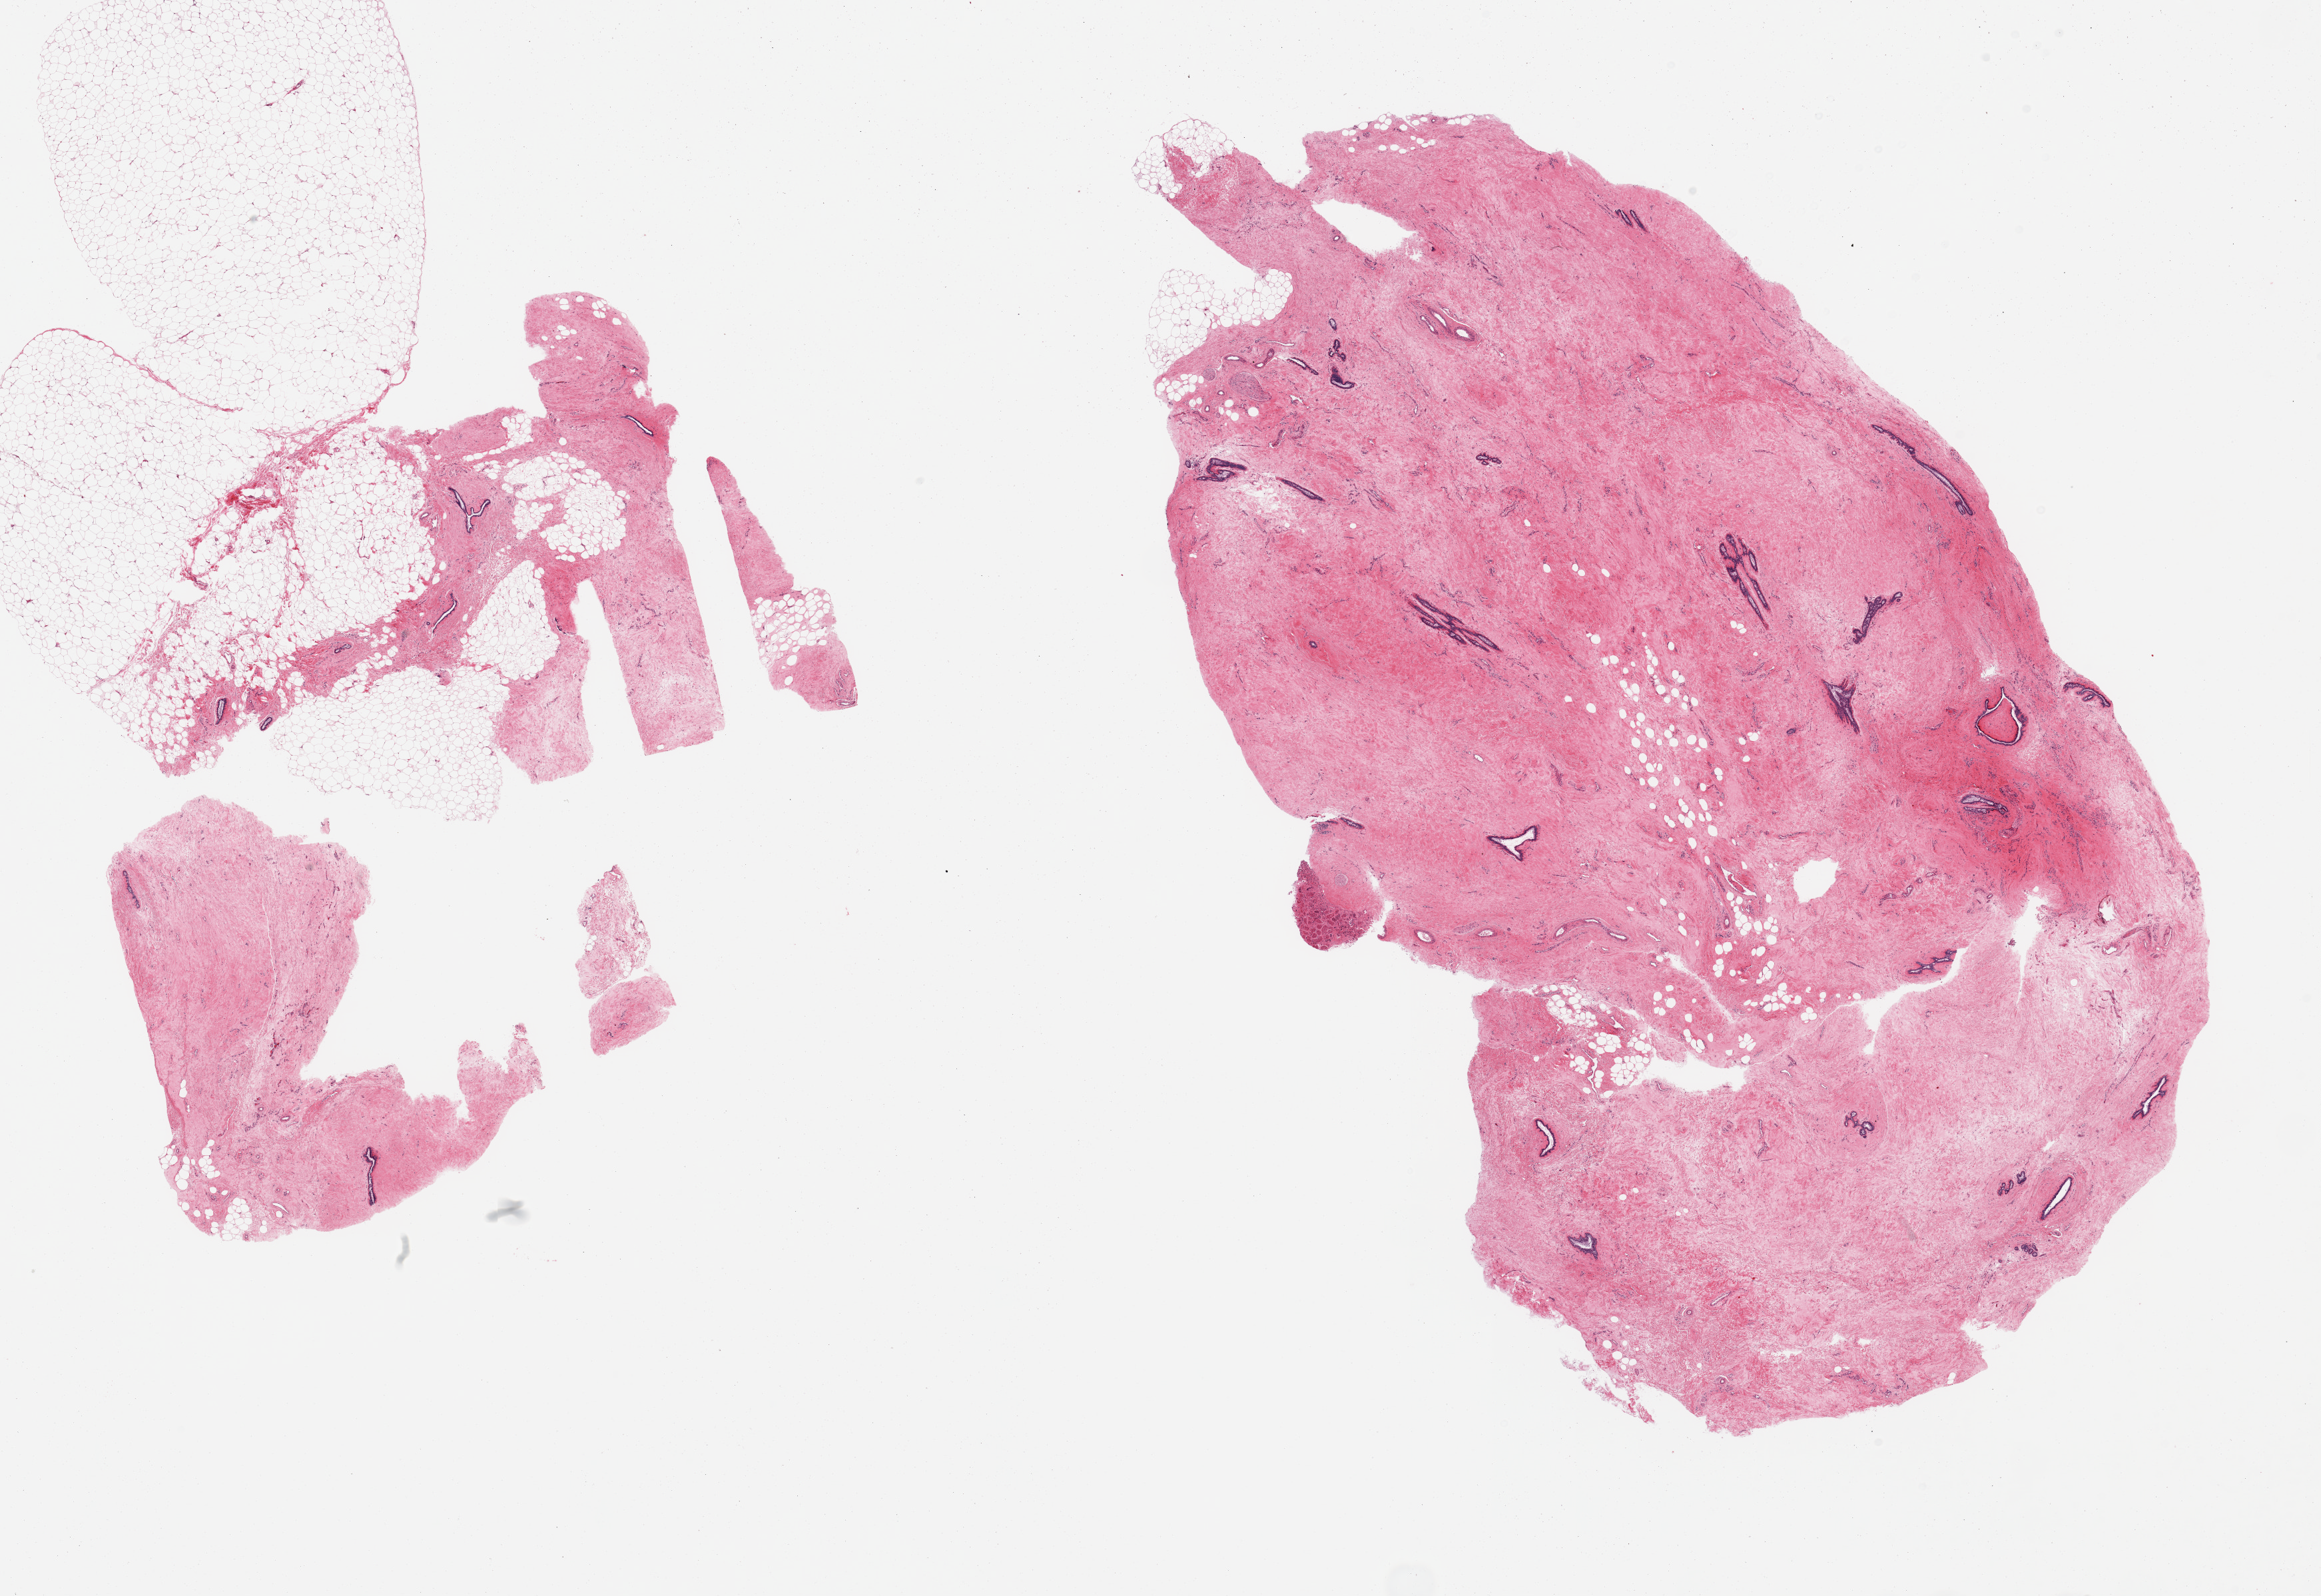
Digitized H&E-stained section — whole scanned area (about 27.6 x 19.0 mm, slide scanned at 20x) shown as a low-resolution overview; PAXgene-fixed paraffin-embedded (PFPE) section; sampled site (target tissue): breast; tissue donor sample. Donor sex: male.
Review note (as recorded): 2 pieces; gynecomastial changes: fibrosis and ducts.